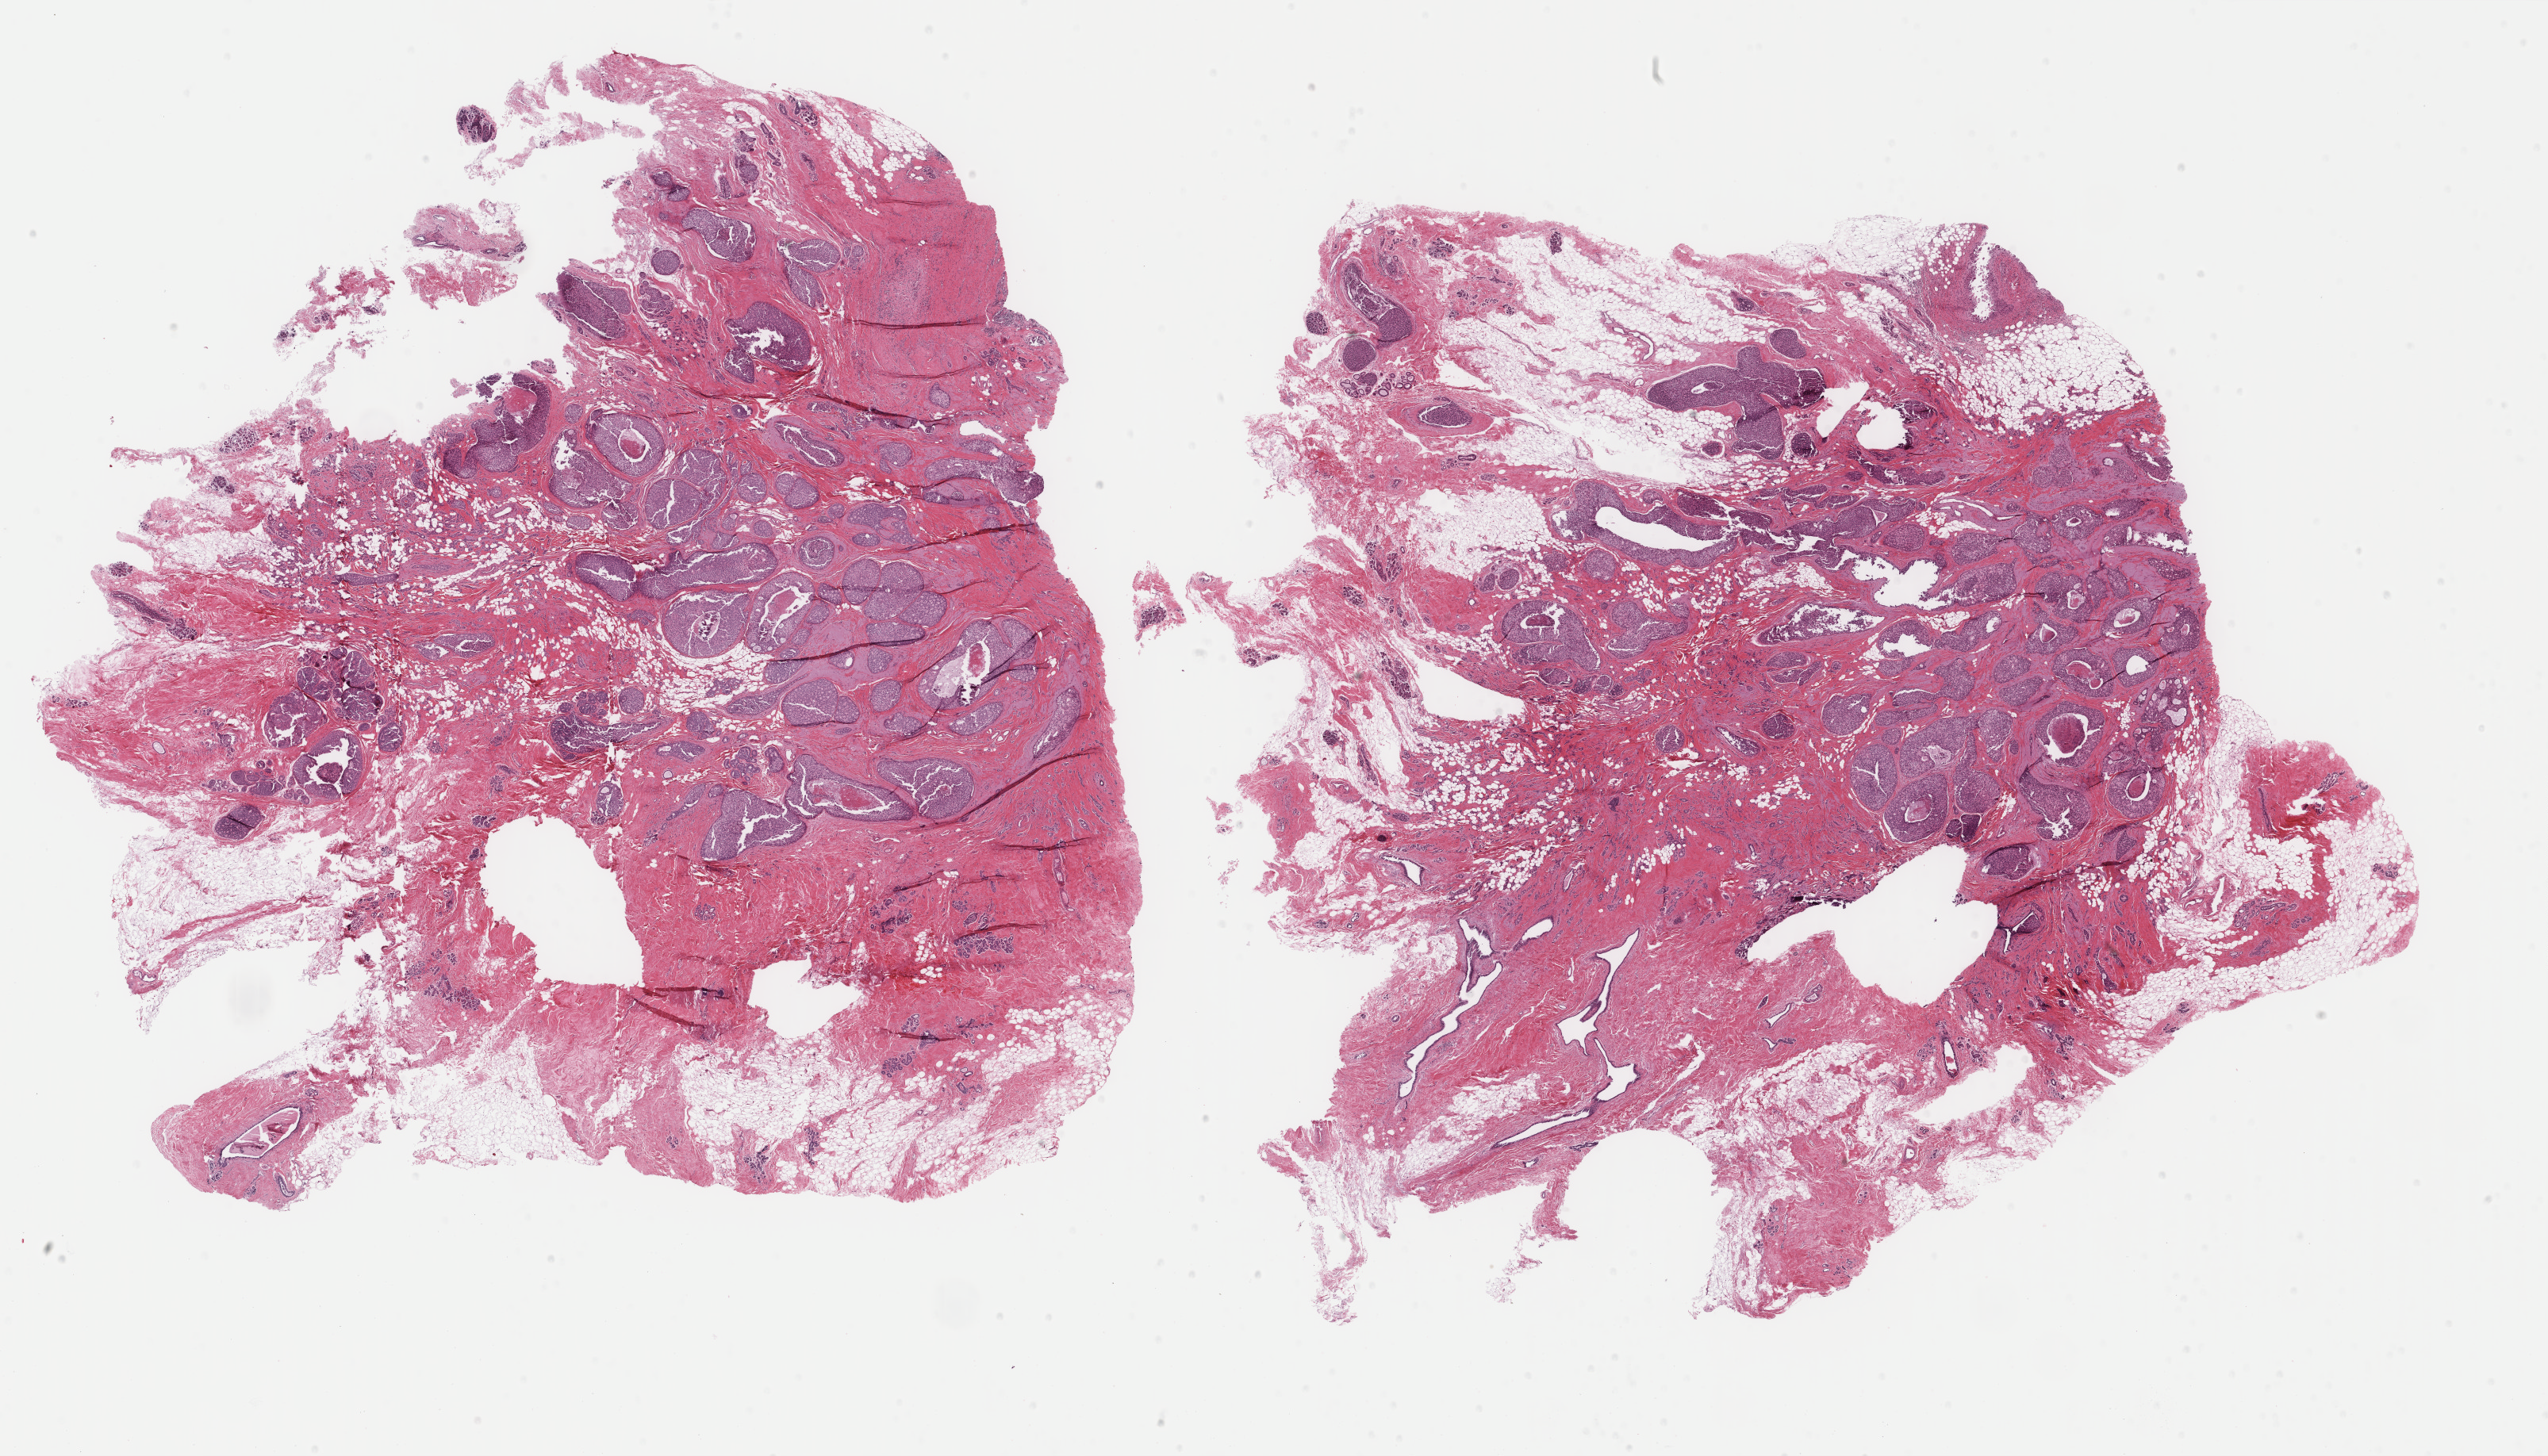
Hematoxylin and eosin (H&E) stained whole-slide image — whole scanned area (about 25.5 x 14.6 mm, acquisition: 40x scan) shown as a low-resolution overview; formalin-fixed paraffin-embedded (FFPE) diagnostic section; primary tumour sample from the breast. Female patient; age at initial diagnosis 55 years.
Diagnosis: Infiltrating duct carcinoma, NOS.